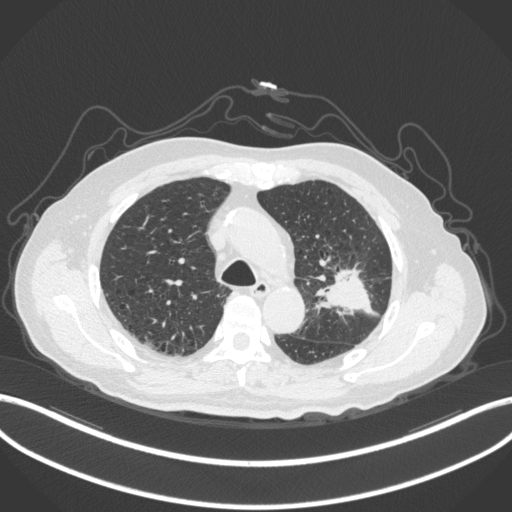
Chest CT, one axial slice; reconstruction kernel B31f; 120 kVp; lung window (W 1500 / L -600 HU); 1 mm slice thickness; 512 × 512 image matrix, field of view 400 × 400 mm. Patient: male, 79 years. Case-level facts recorded for this patient, not image findings: clinical TNM (as recorded): T2a N1 M1.
Outlined on this slice (bounding box drawn by a radiologist):
- lung tumour (recorded histology: adenocarcinoma): bounding box [x1, y1, x2, y2] px = [308, 260, 381, 318]